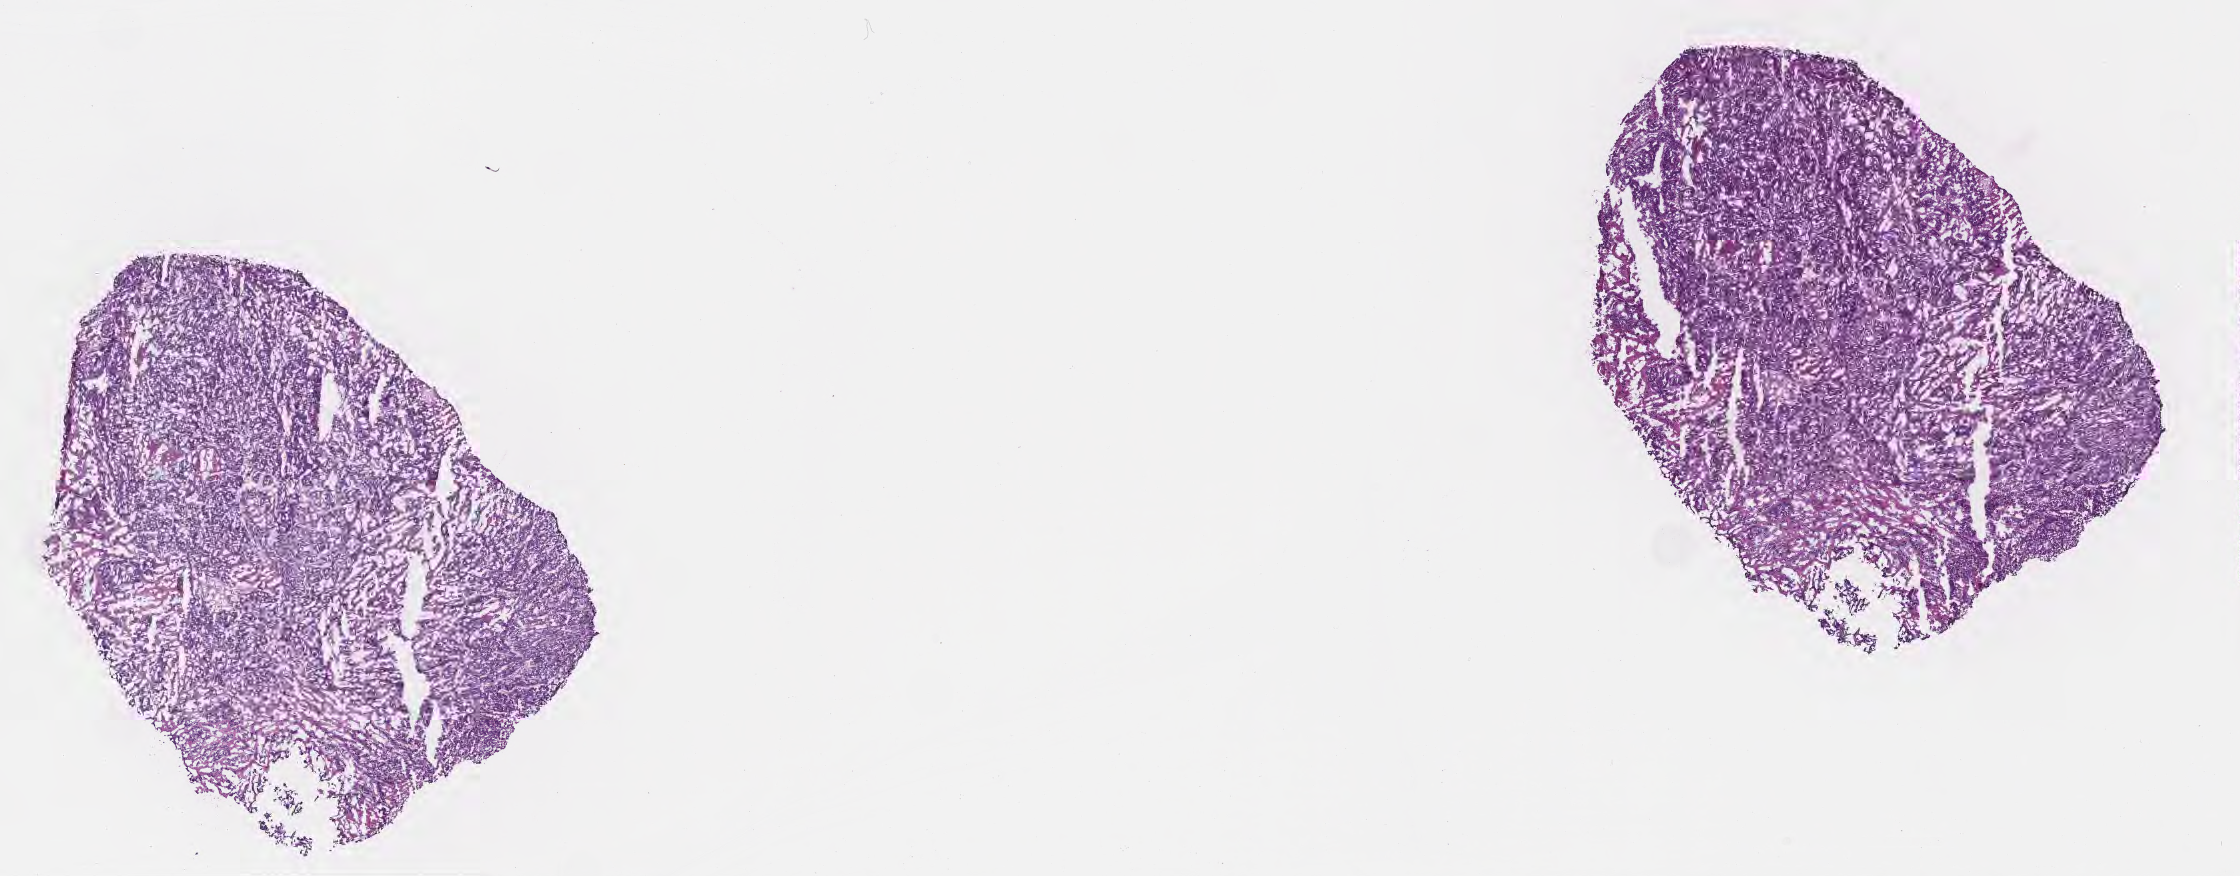
H&E whole-slide image, a low-resolution overview of the entire scanned area, about 18.1 x 7.1 mm, frozen section (tissue freezing medium), specimen: metastatic tumor tissue, resected from brain. Patient: female, age at initial diagnosis 47 years. Composition of this section per pathologist review: tumor cells 60%, tumor nuclei 60%, stromal cells 25%, necrosis 5%, normal cells 10%. Inflammatory infiltration, as recorded: lymphocyte infiltration 5%, monocyte infiltration 0%, neutrophil infiltration 2%.
Patient diagnosis (primary): Adenocarcinoma, NOS.